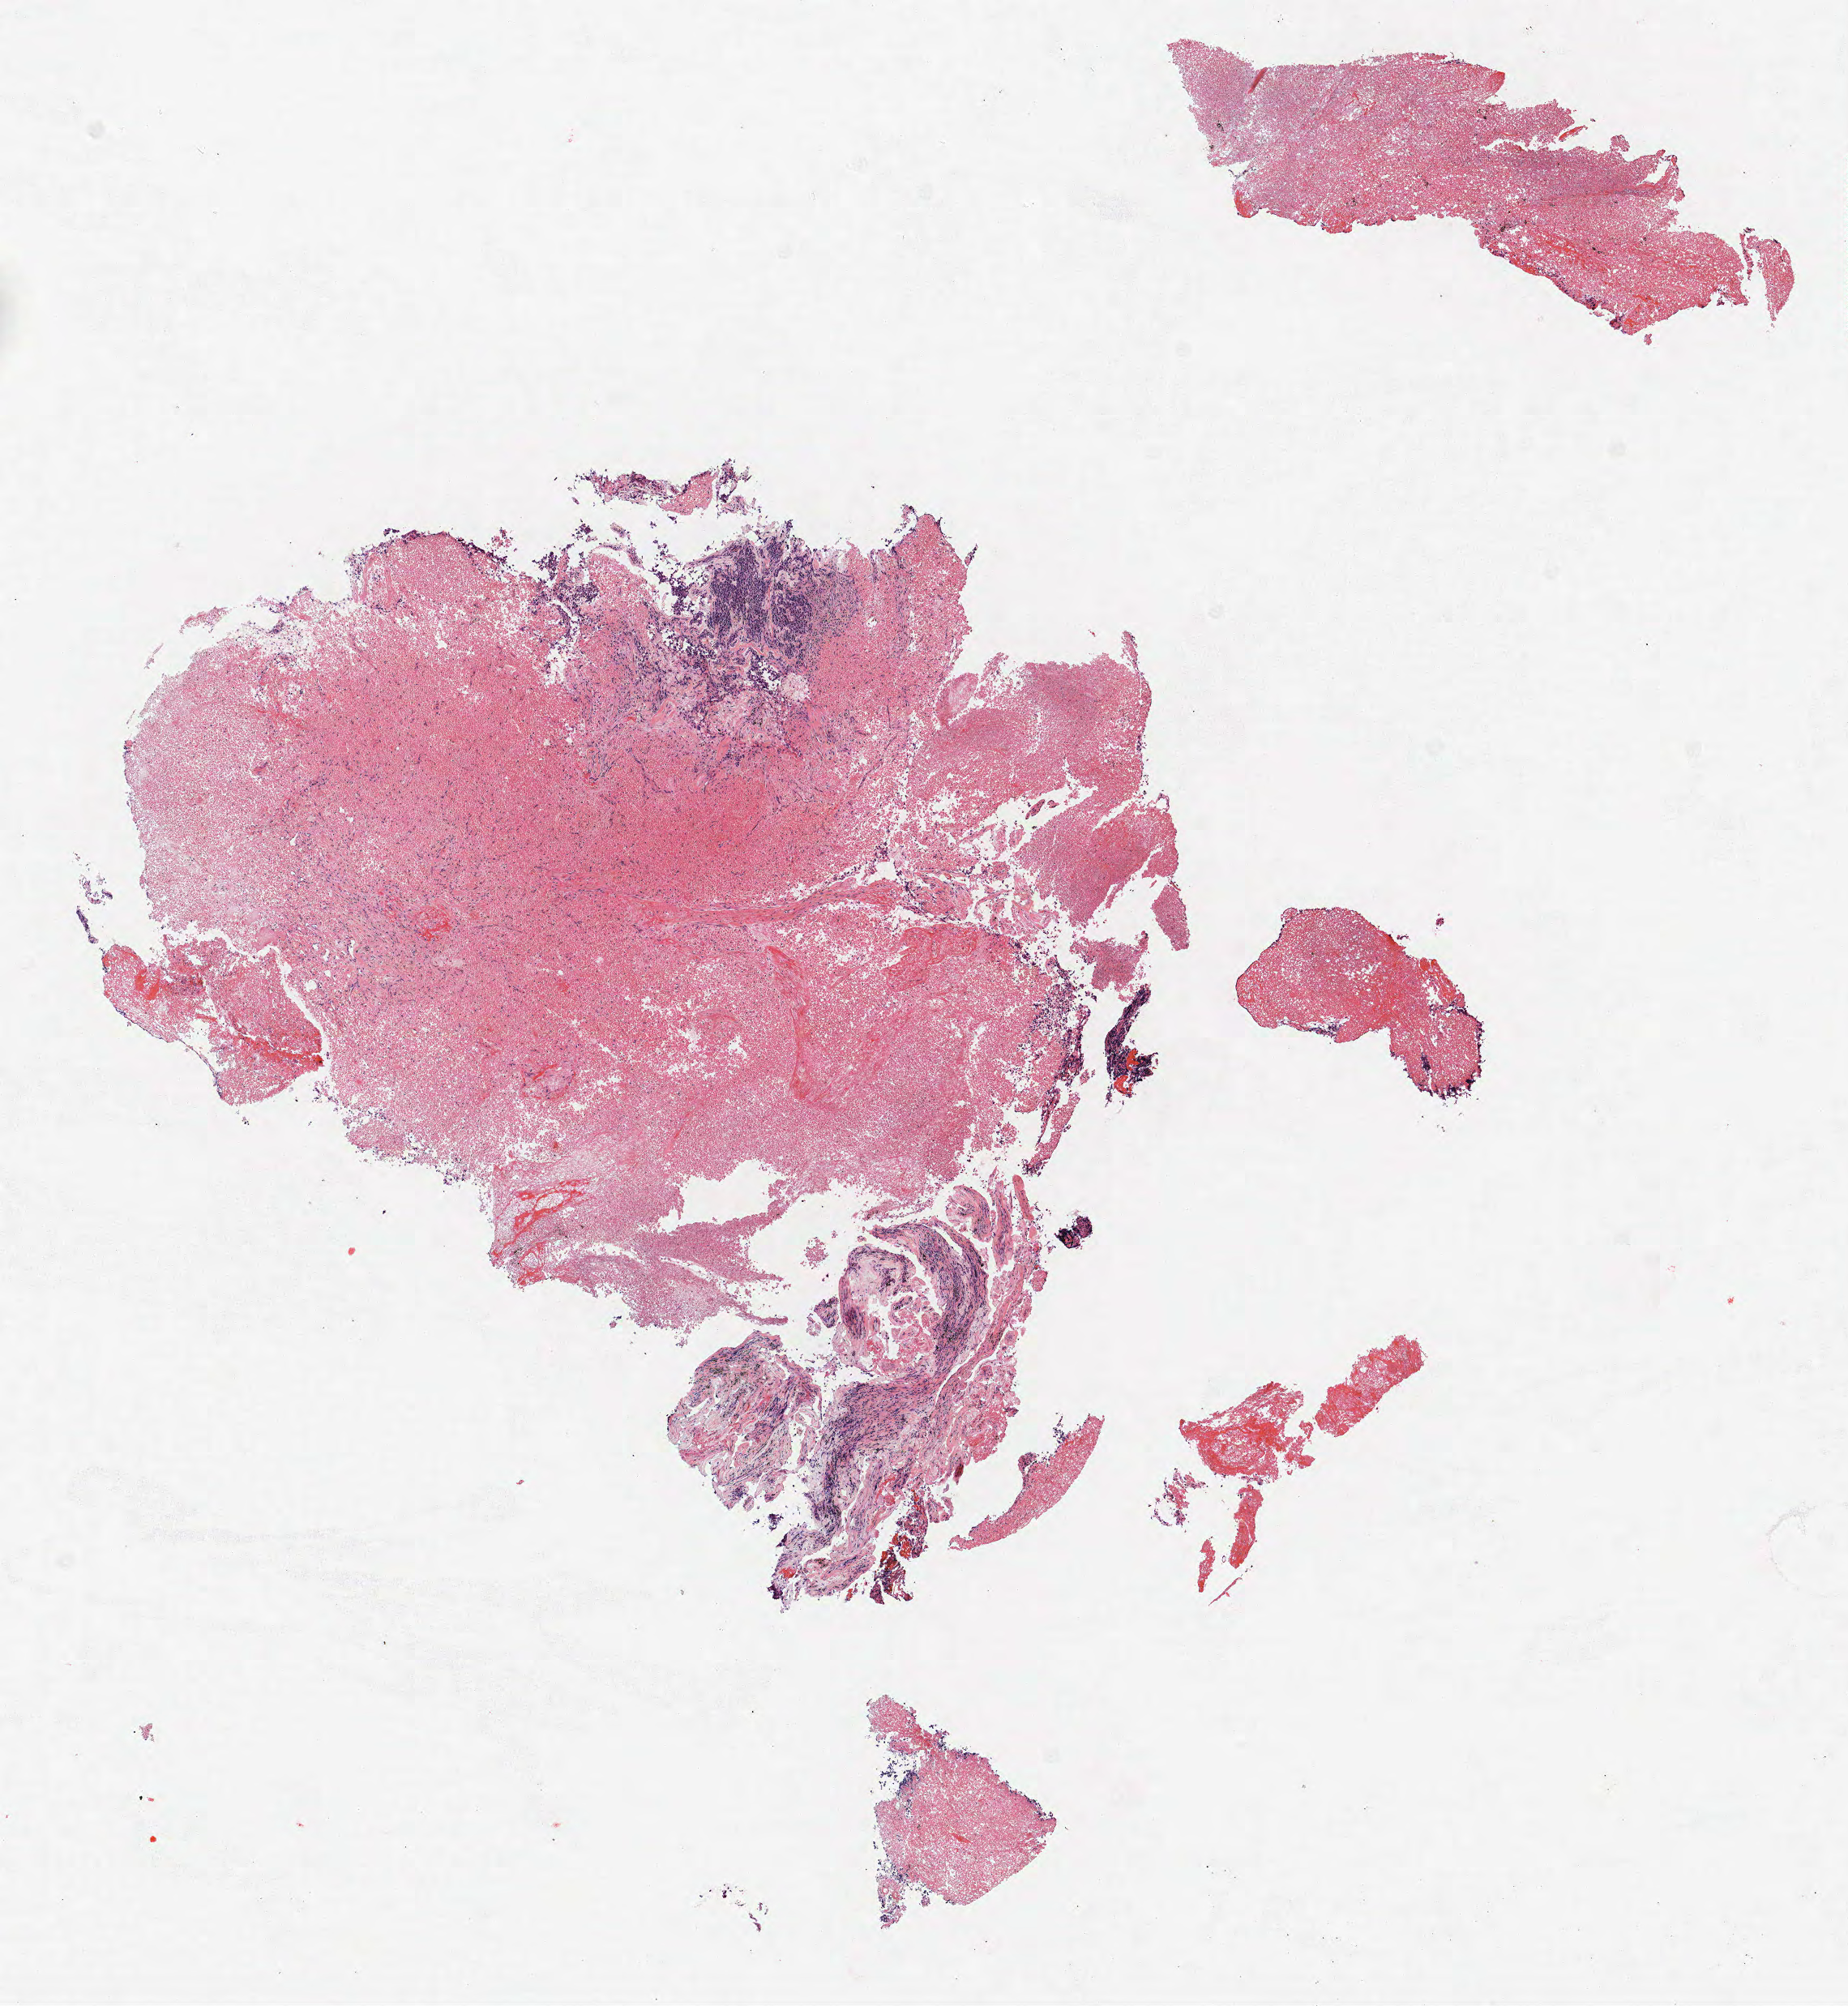
Hematoxylin and eosin (H&E) stained whole-slide image, whole scanned area (about 9.1 x 9.9 mm, acquisition: 40x scan) shown as a low-resolution overview. FFPE section. Lung. Male, age 62 at enrolment. Grade: poorly differentiated (G3).
Participant's lung-cancer diagnosis: Squamous cell carcinoma, NOS. ICD-O-3 topography: lung, NOS (C34.9). Stage (AJCC 6th edition): IV.